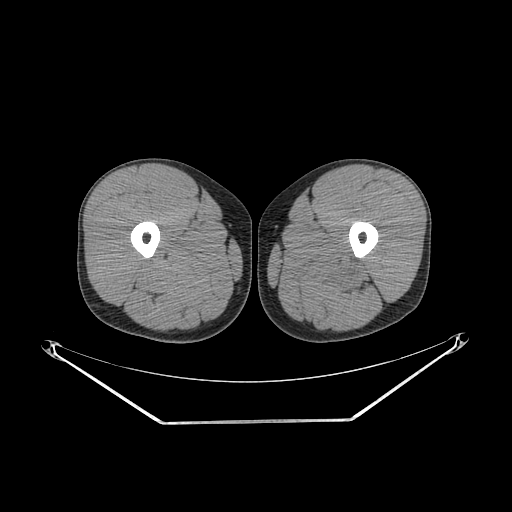
CT of an extremity soft-tissue mass (from a PET/CT study), one axial slice; slice 237 of 267 in the series (ordered by position); reconstruction kernel SOFT; 140 kVp; soft-tissue window (W 400 / L 40 HU); 512 × 512 image matrix, field of view 500 × 500 mm. Male patient. Case-level facts recorded for this patient, not image findings: histological type: extraskeletal osteosarcoma; grade: high; site of the primary tumour: left adductur.
Outlined on this slice (expert contour drawn on MRI and transferred to this co-registered scan by the dataset authors):
- gross tumour volume (mass): bounding box (x1, y1, x2, y2) in pixels: (274, 247, 380, 295)